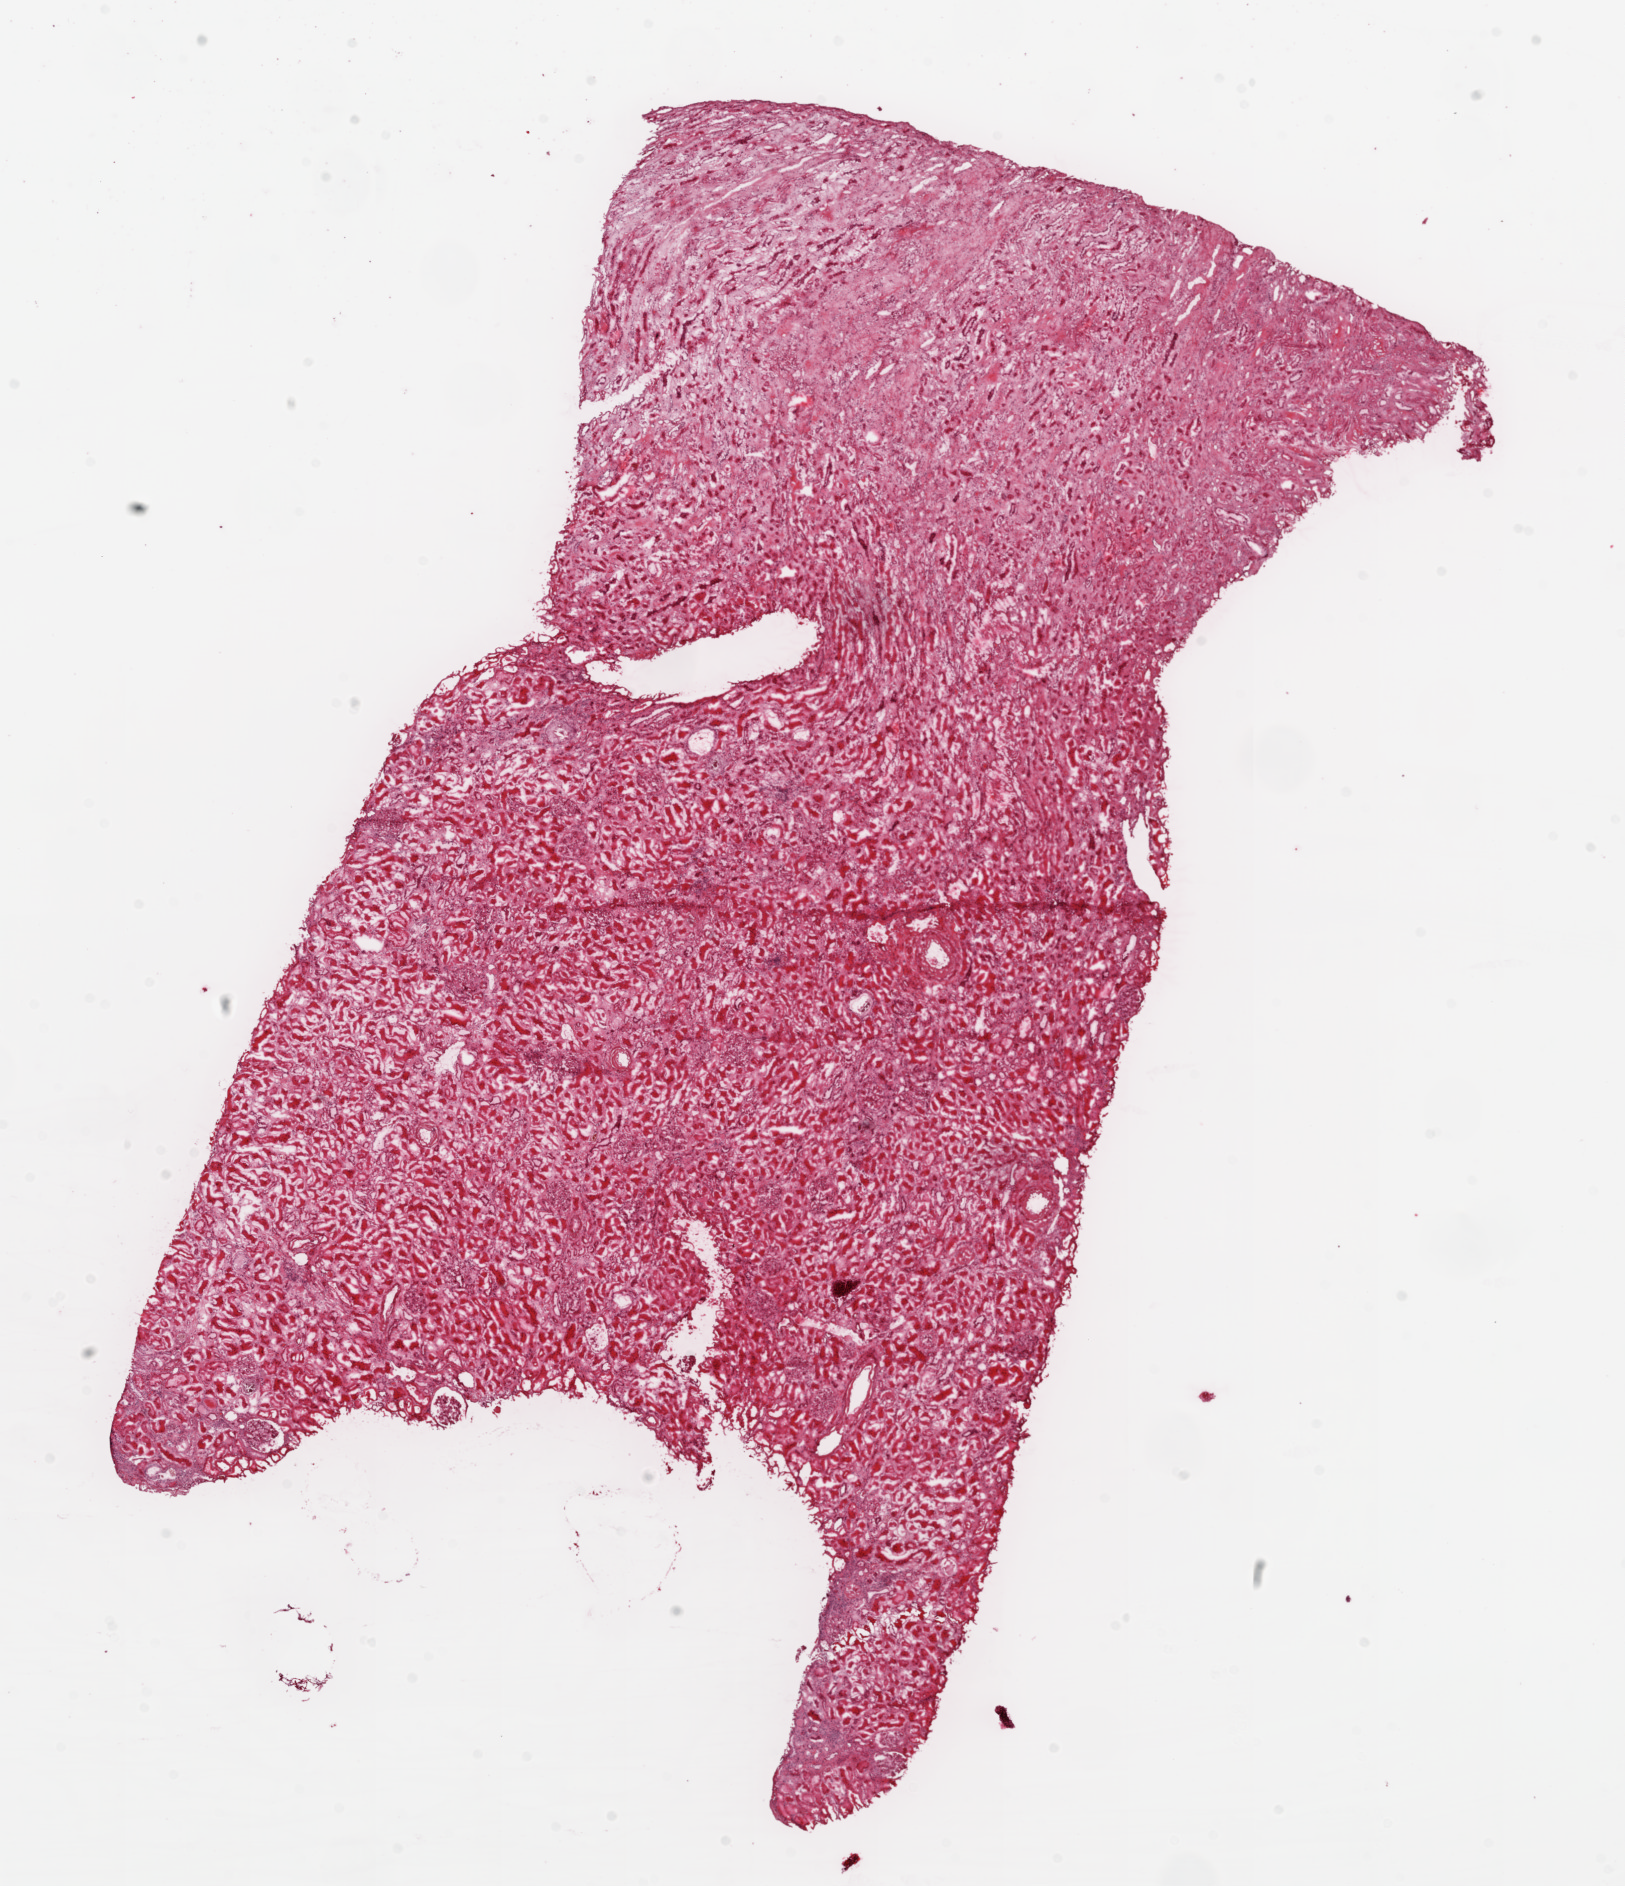
H&E-stained whole-slide image, whole scanned area (about 13.0 x 15.1 mm, acquisition: 20x scan) shown as a low-resolution overview, frozen section from the top of the tissue portion, solid tissue normal (non-tumour tissue) sample from the kidney. Patient: male, age at initial diagnosis 76 years.
• this section: solid tissue normal (non-tumour) sample from the same patient
• patient diagnosis: Clear cell adenocarcinoma, NOS